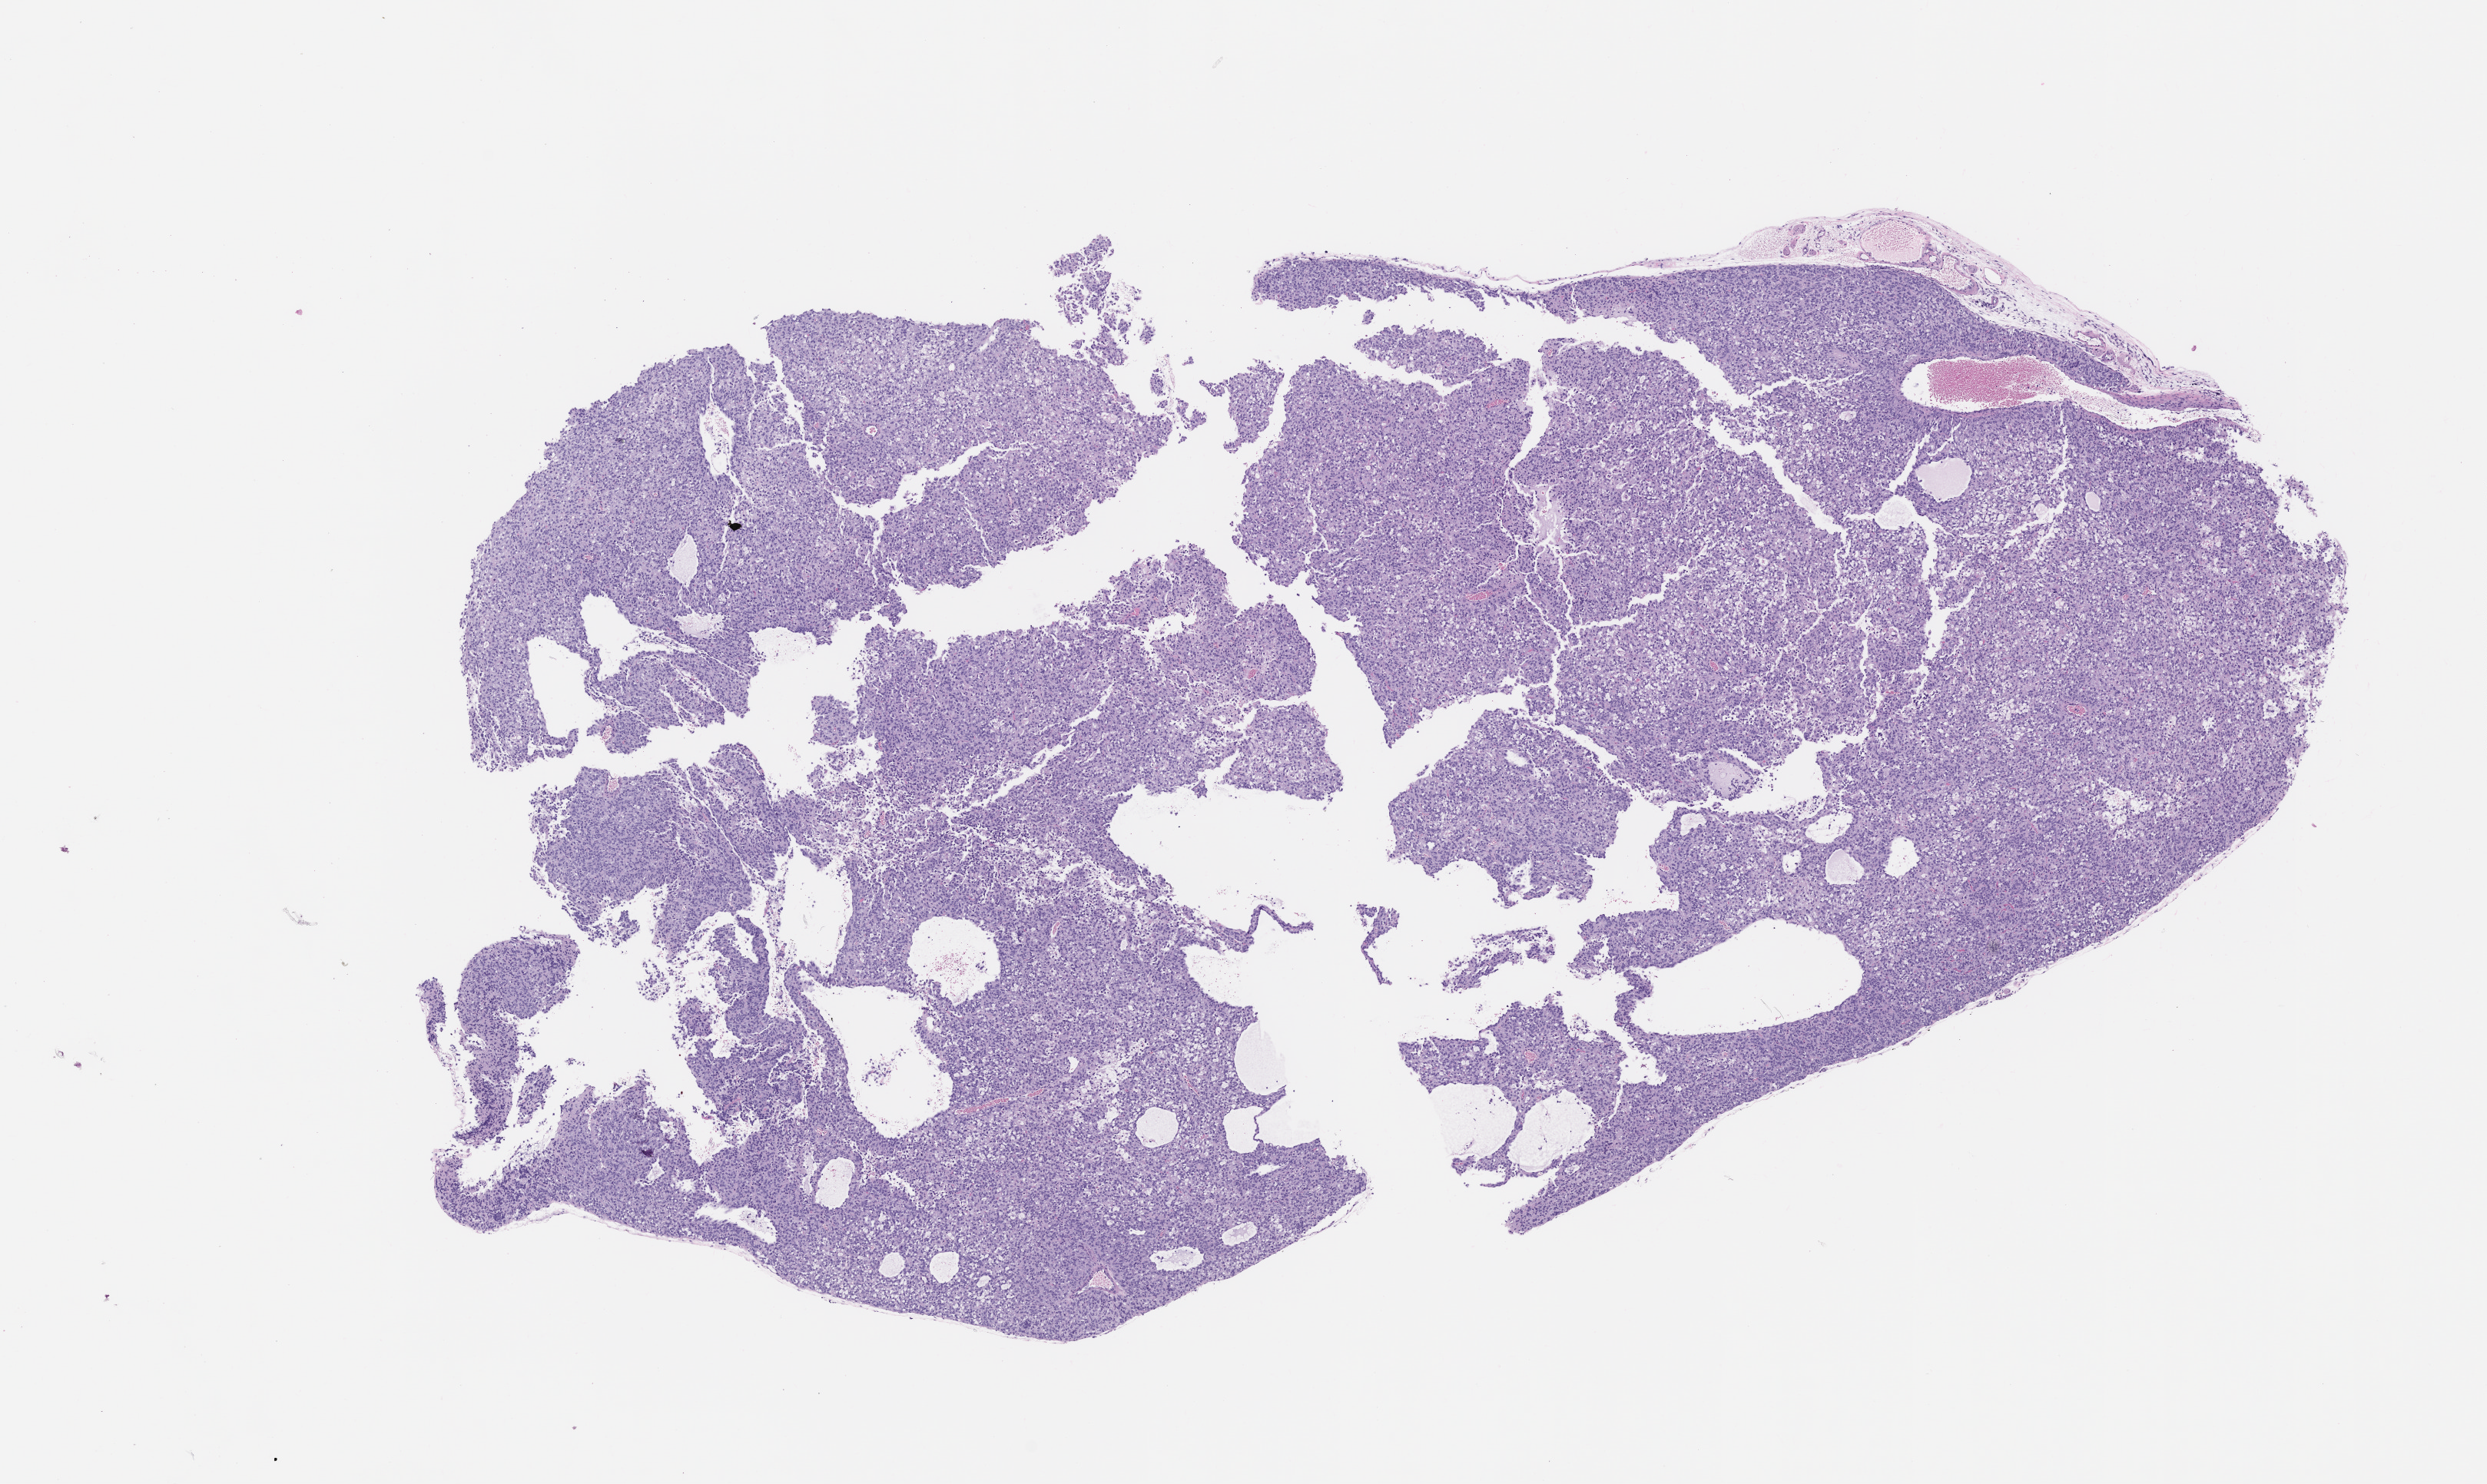
Whole-slide image, H&E: patient-derived xenograft (human tumor grown in a mouse), passage 2 — a low-resolution overview of the entire scanned area, about 13.0 x 7.8 mm; FFPE section; tumor site category: uterus.
- originating patient diagnosis: Leiomyosarcoma